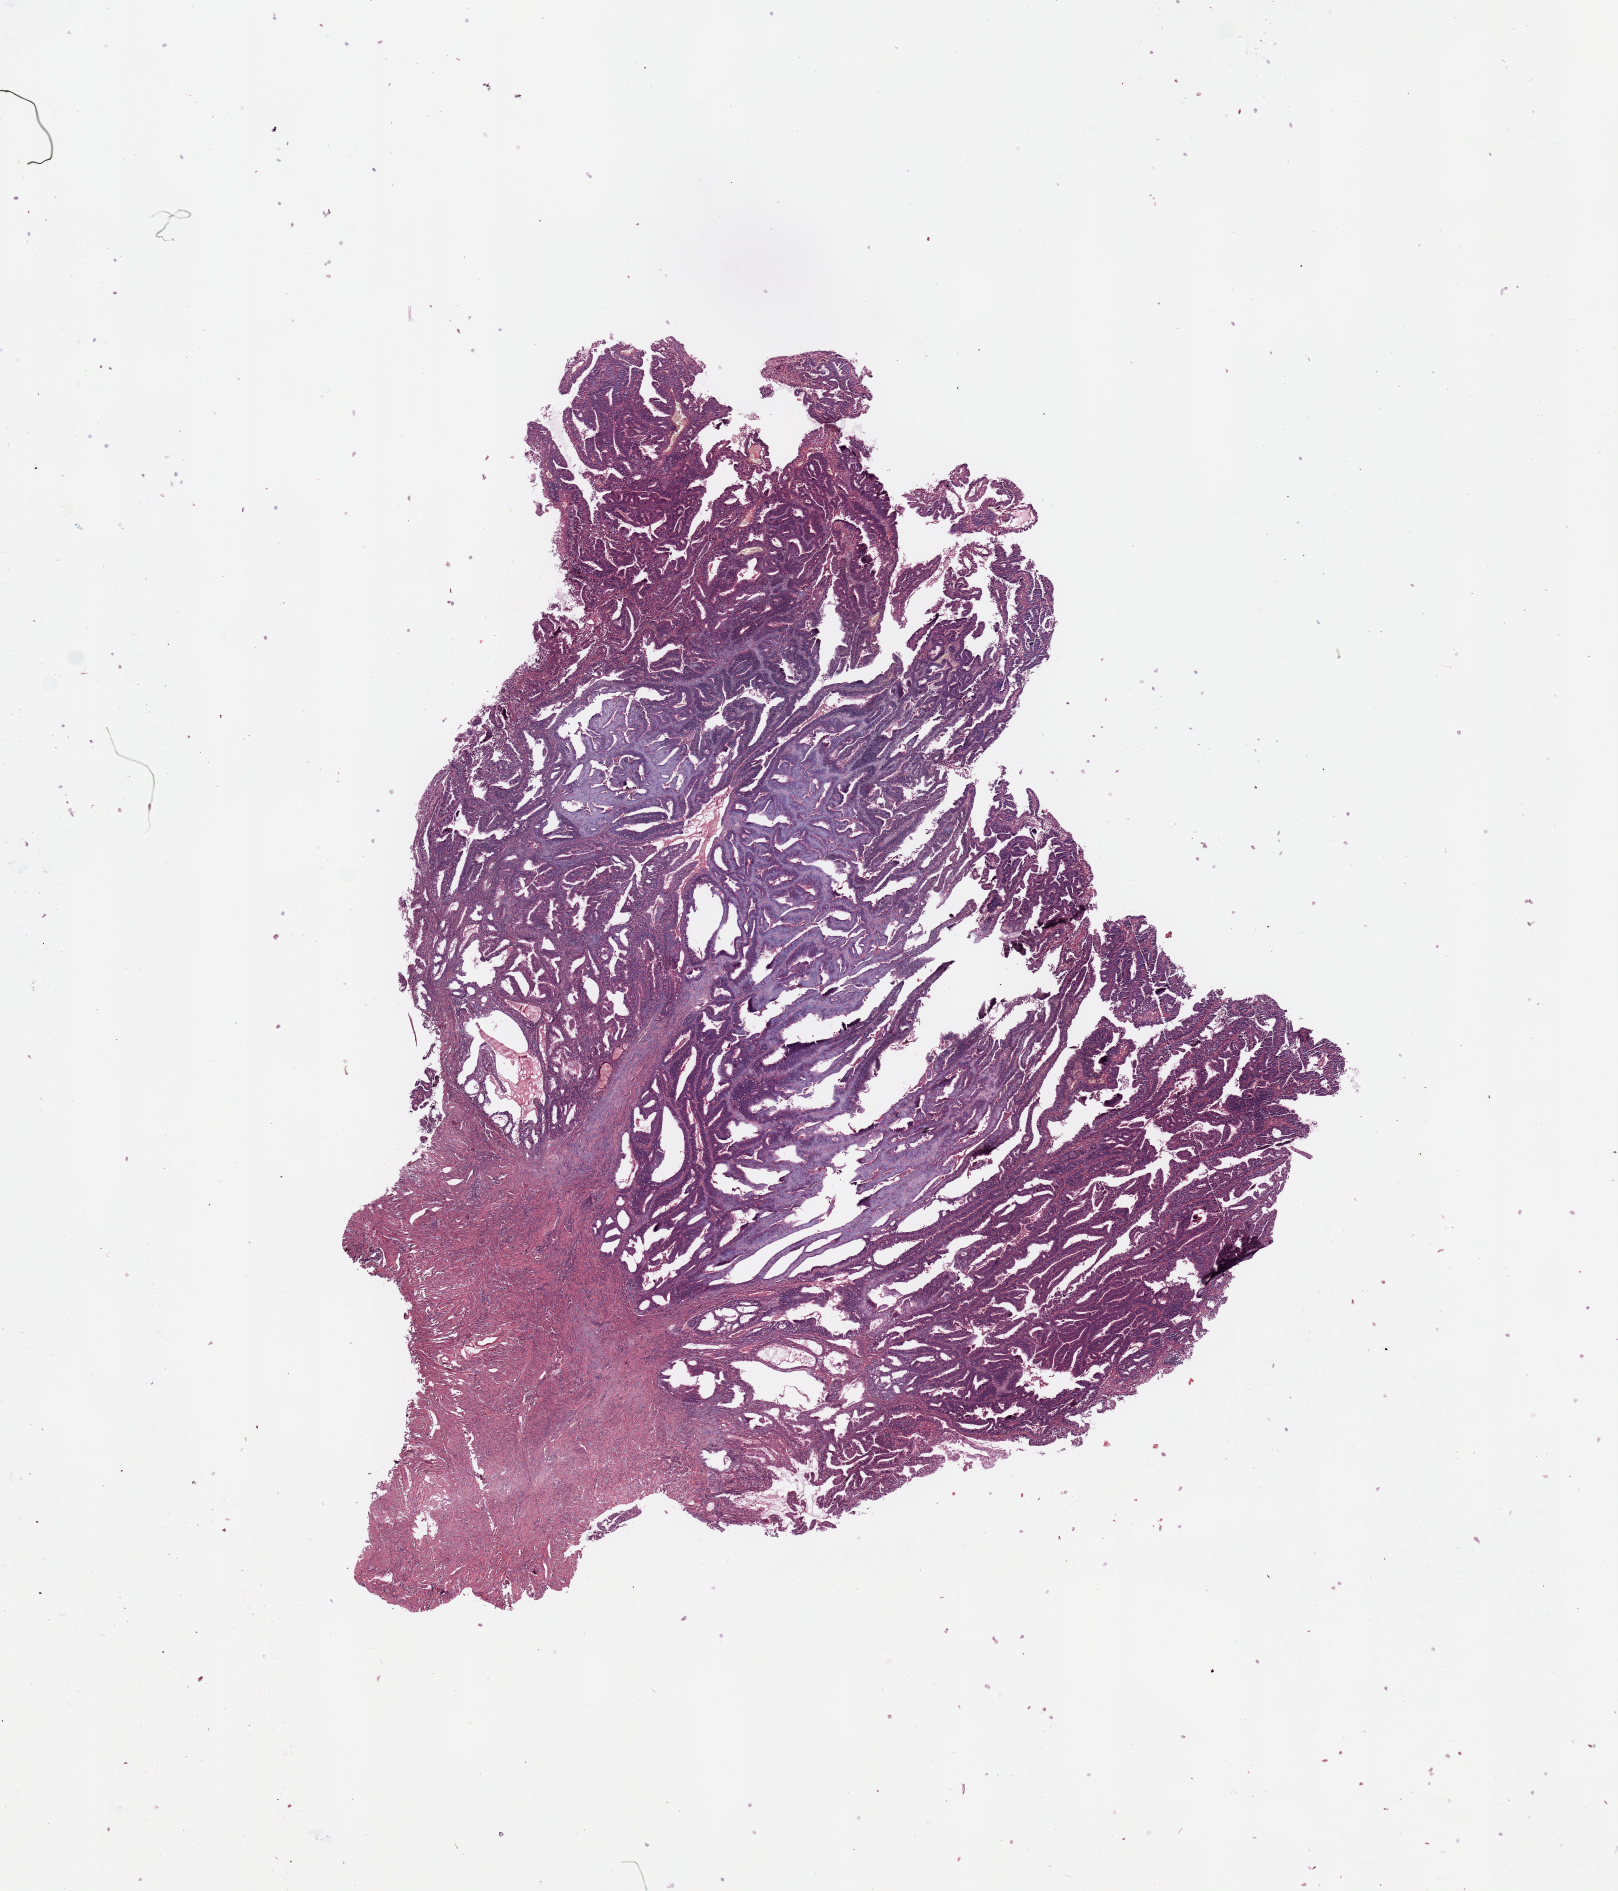
Digitized Hematoxylin and eosin (H&E) stained tissue section (whole slide) — shown as a low-resolution overview of the whole scanned area (about 12.8 x 15.0 mm), tumour tissue sample, uterus. 57-year-old female patient. Histologic grade: G1 (well differentiated).
AJCC pathologic stage: I. Diagnosis: Endometrioid adenocarcinoma, NOS.